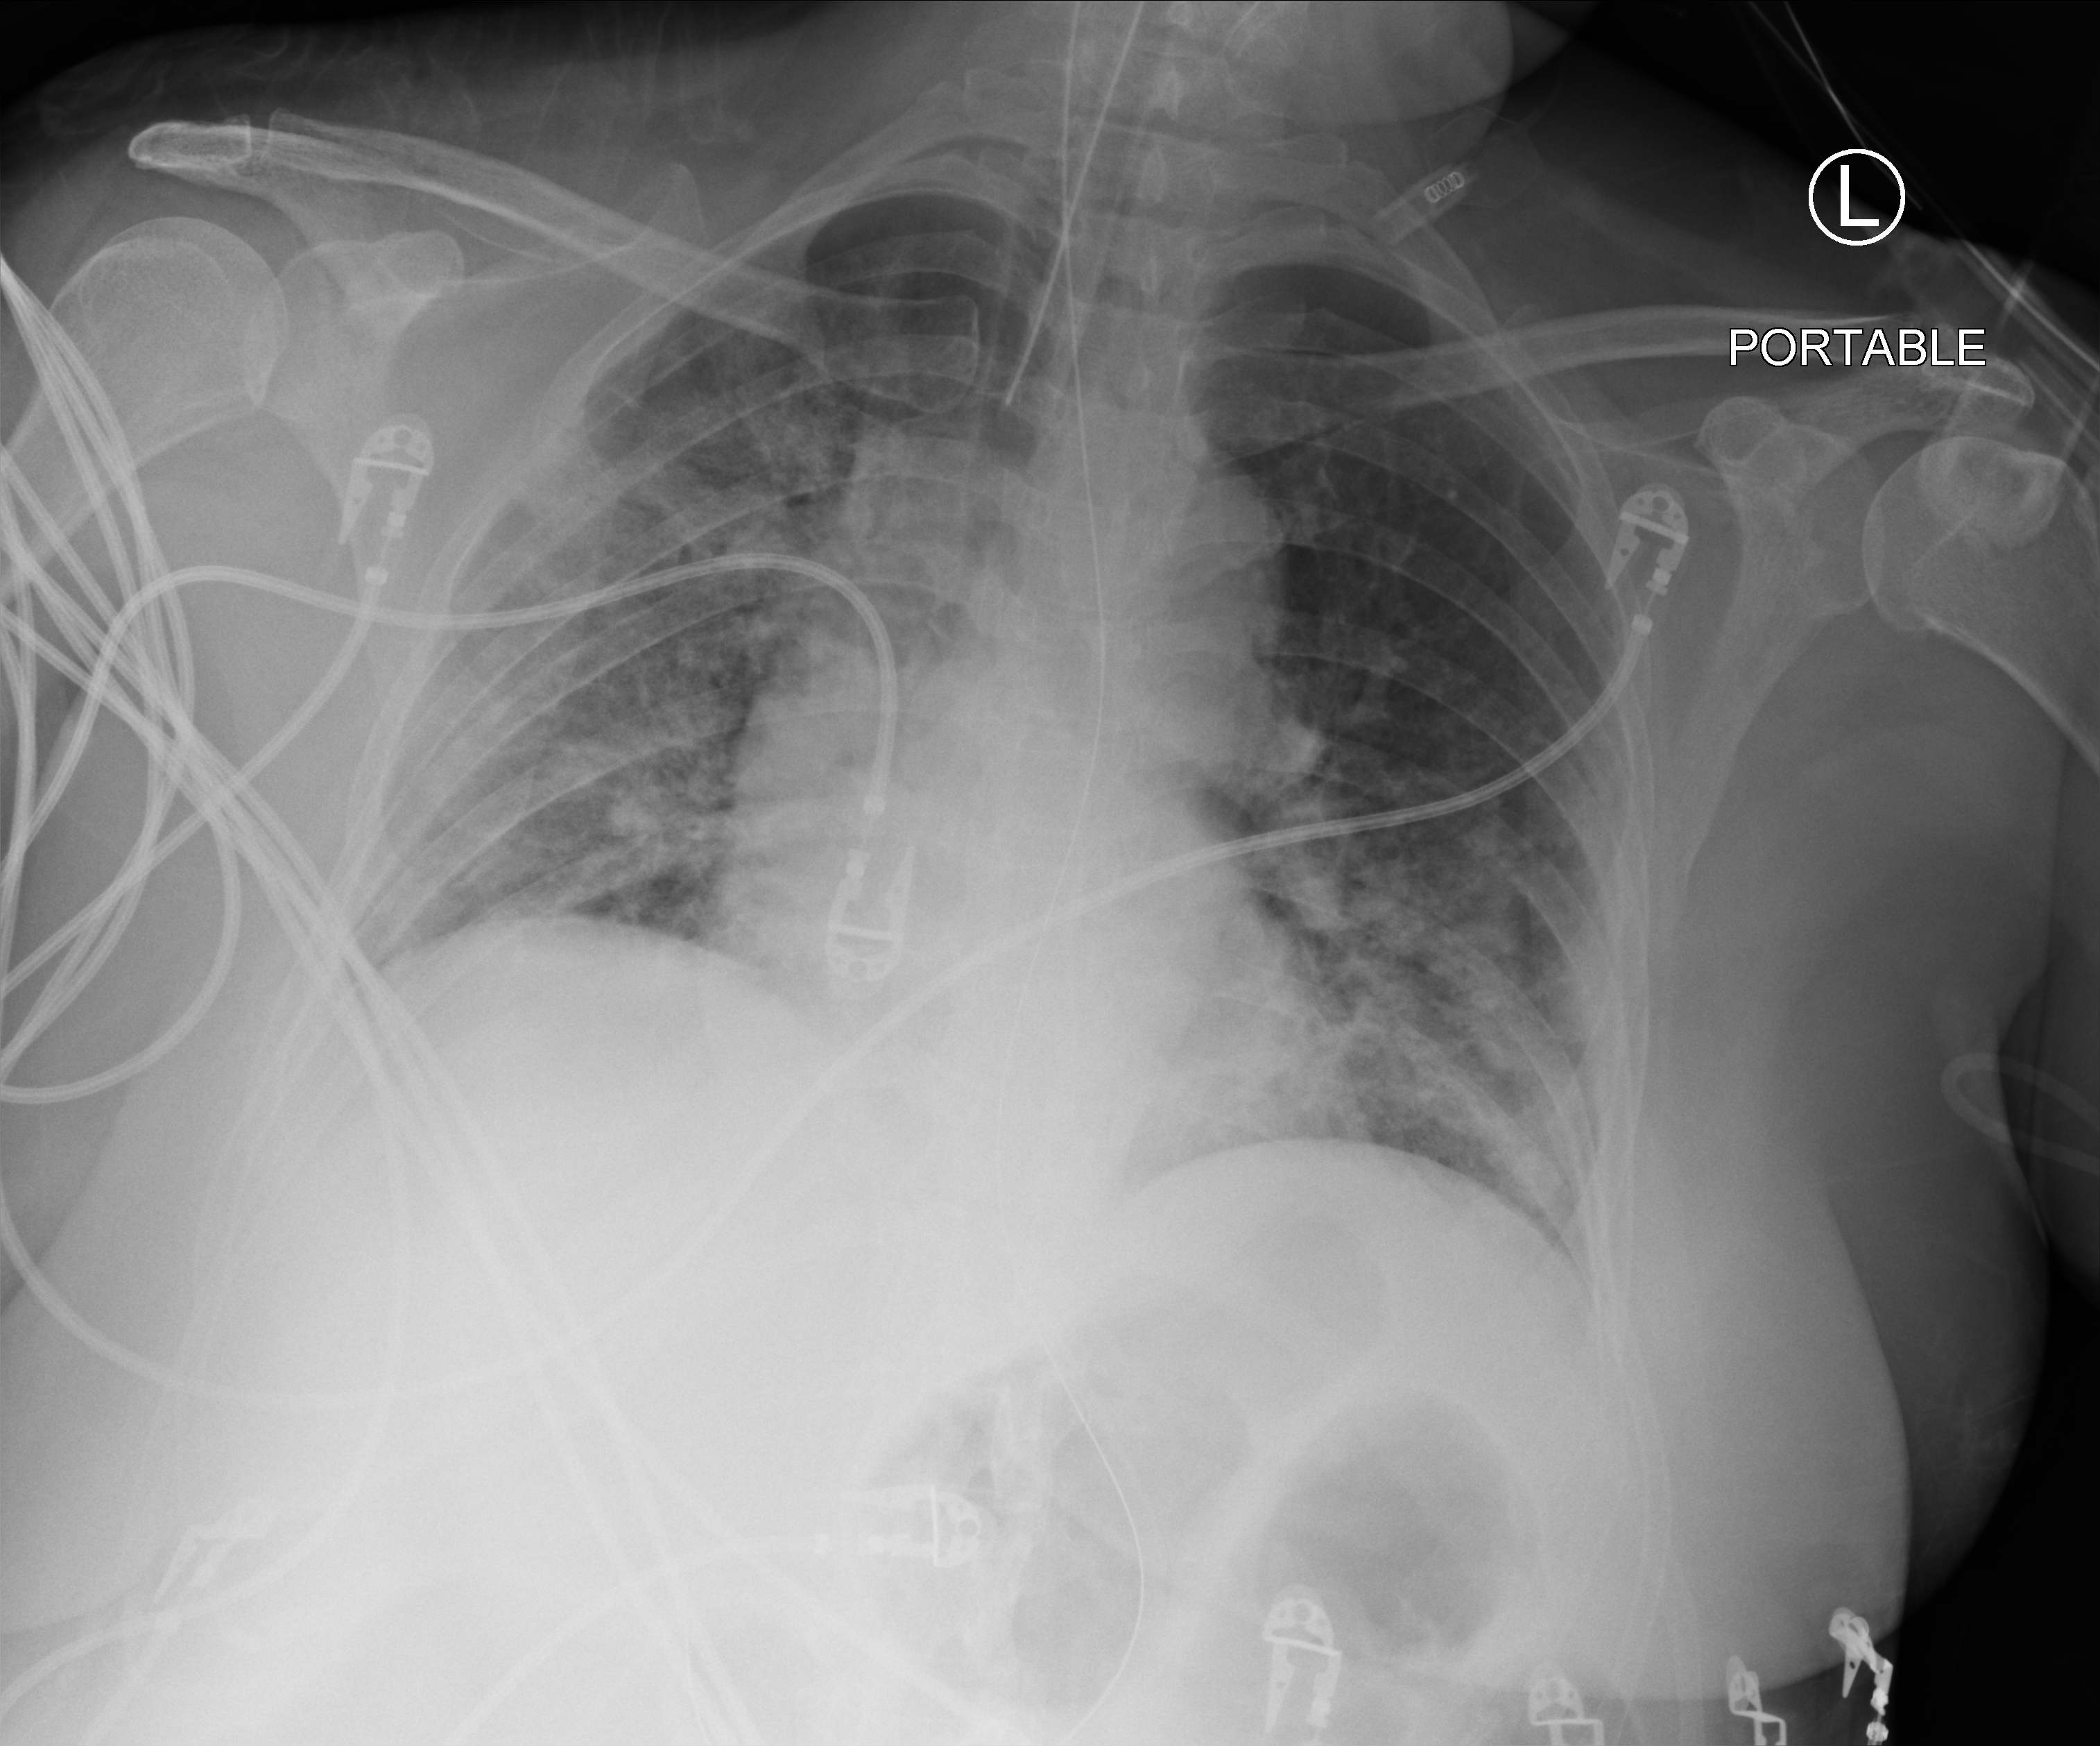
Chest X-ray (portable); anteroposterior (AP) projection. Patient hospitalised with COVID-19; female, aged 18–59 years.
Hospital-stay facts (about this admission, not read from this image; timing relative to this image not recorded): length of hospital stay: 22 days.